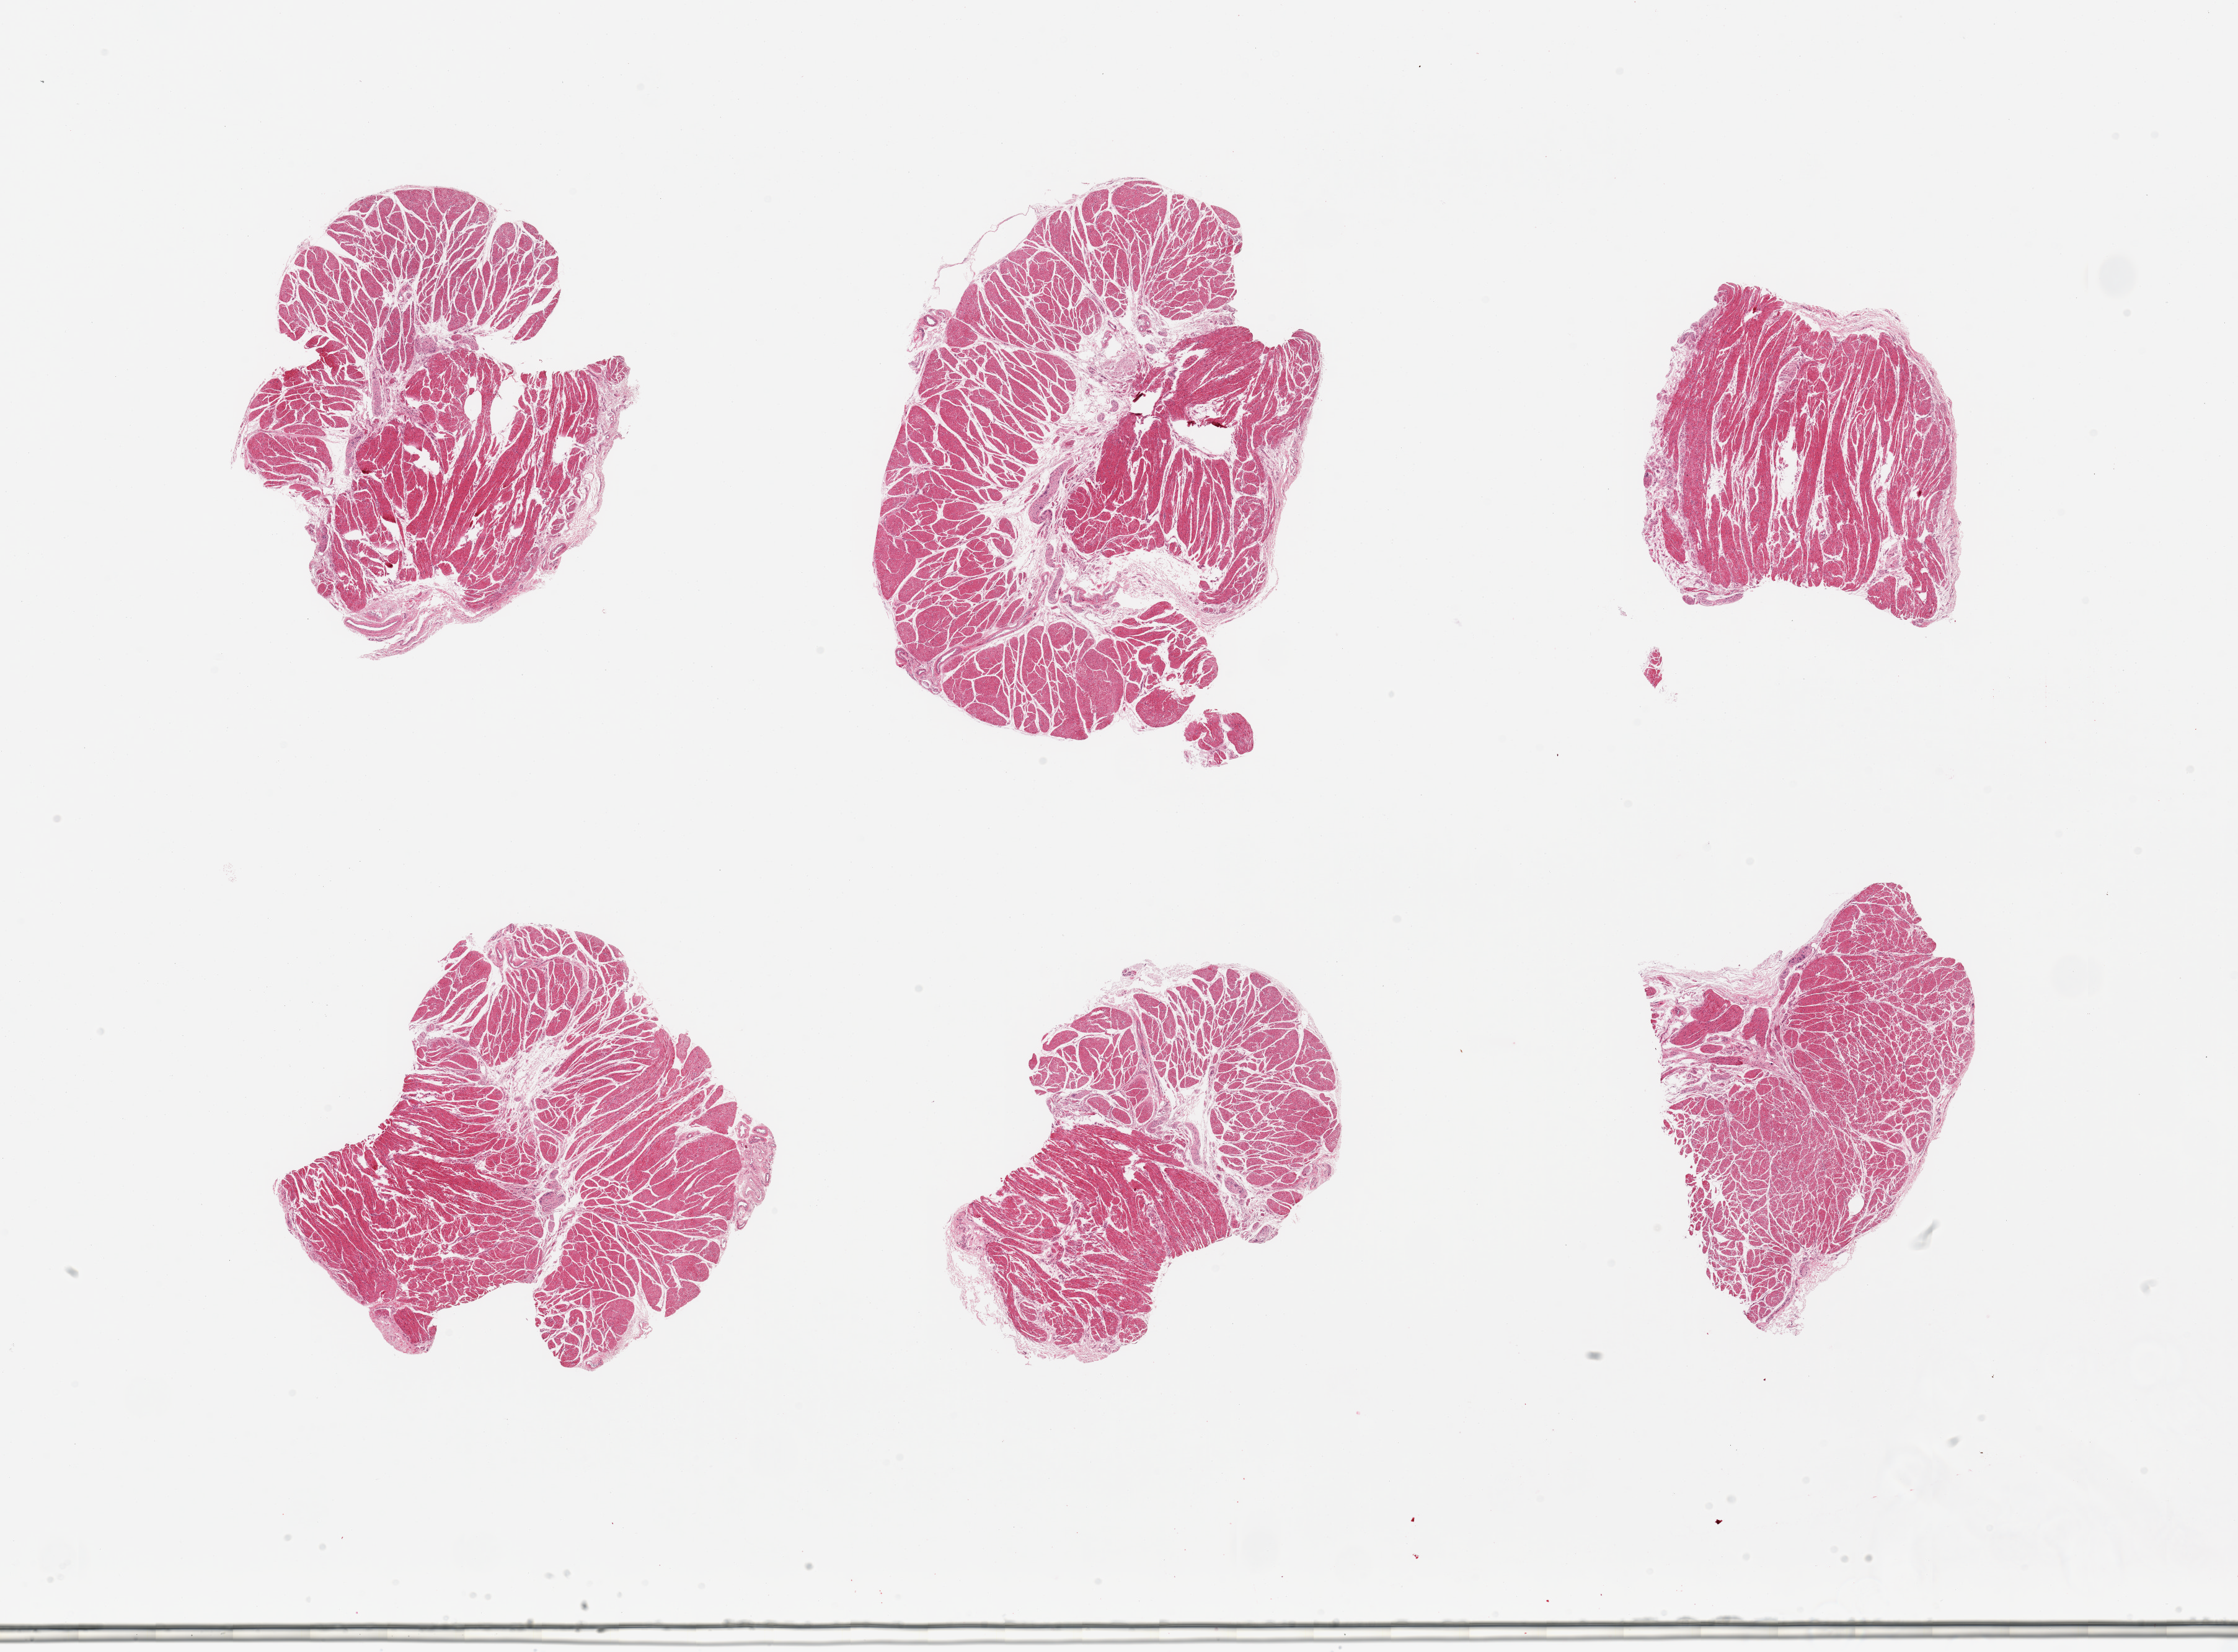
Digitized hematoxylin and eosin (H&E)-stained section — low-resolution overview of the scanned area, about 28.5 x 21.1 mm (from a 20x scan). PAXgene-fixed, paraffin-embedded tissue. Target tissue: esophageal muscle. Tissue donor sample. Donor sex: female.
* pathologist's review note for this sample: 6 pieces; well trimmed